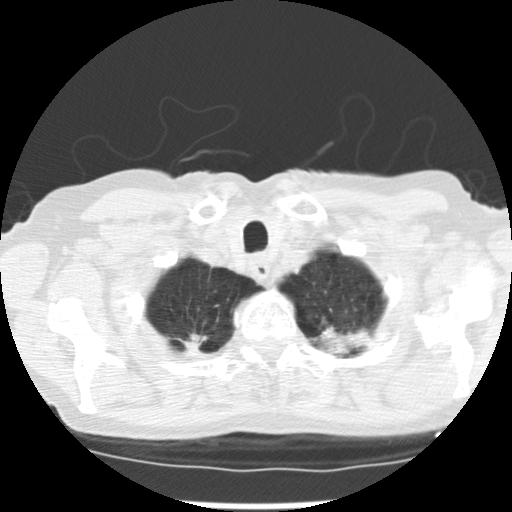
Chest CT (low-dose screening protocol), one axial image. First (baseline) screen. Lung window (W 1500 / L -600 HU). Standard (soft-tissue) reconstruction kernel (STANDARD). Slice 19 of 265 in the series. 512 × 512 image matrix. Female participant, aged 72 years at enrolment.
Expert reader's lesion annotation, bounding box (x1, y1, x2, y2) in pixels: (164, 317, 232, 366). The screening reader recorded 3 non-calcified nodules or masses ≥4 mm on this exam (right upper lobe, left upper lobe, left lower lobe); which of them this box marks is not recorded. Official screen result: positive, change unspecified: nodule(s) >= 4 mm or enlarging nodule(s), mass(es), or other non-specific abnormalities suspicious for lung cancer.